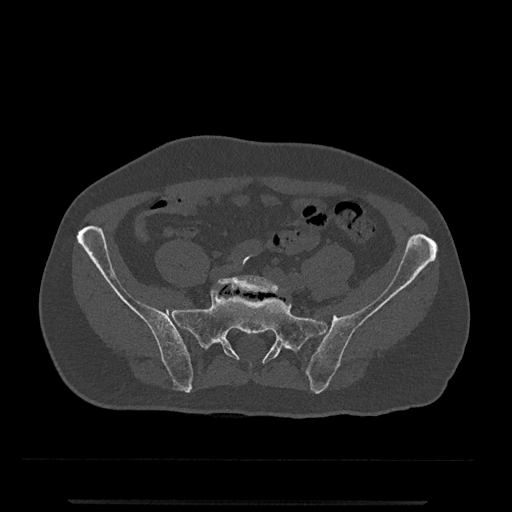
CT including the spine, one axial slice. Slice 20 of 797 in the series (ordered by position). 120 kVp. Bone window (W 1800 / L 400 HU). 0.5 mm slice thickness. 512 × 512 image matrix, field of view 419 × 419 mm. Male patient, age 63 years. Case-level facts recorded for this patient, not image findings: primary cancer: prostate.
Annotated regions visible in this slice (semi-automatic segmentation, software-assisted and operator-edited):
- L5 vertebra: bounding box (x1, y1, x2, y2) in pixels: (216, 275, 282, 295)